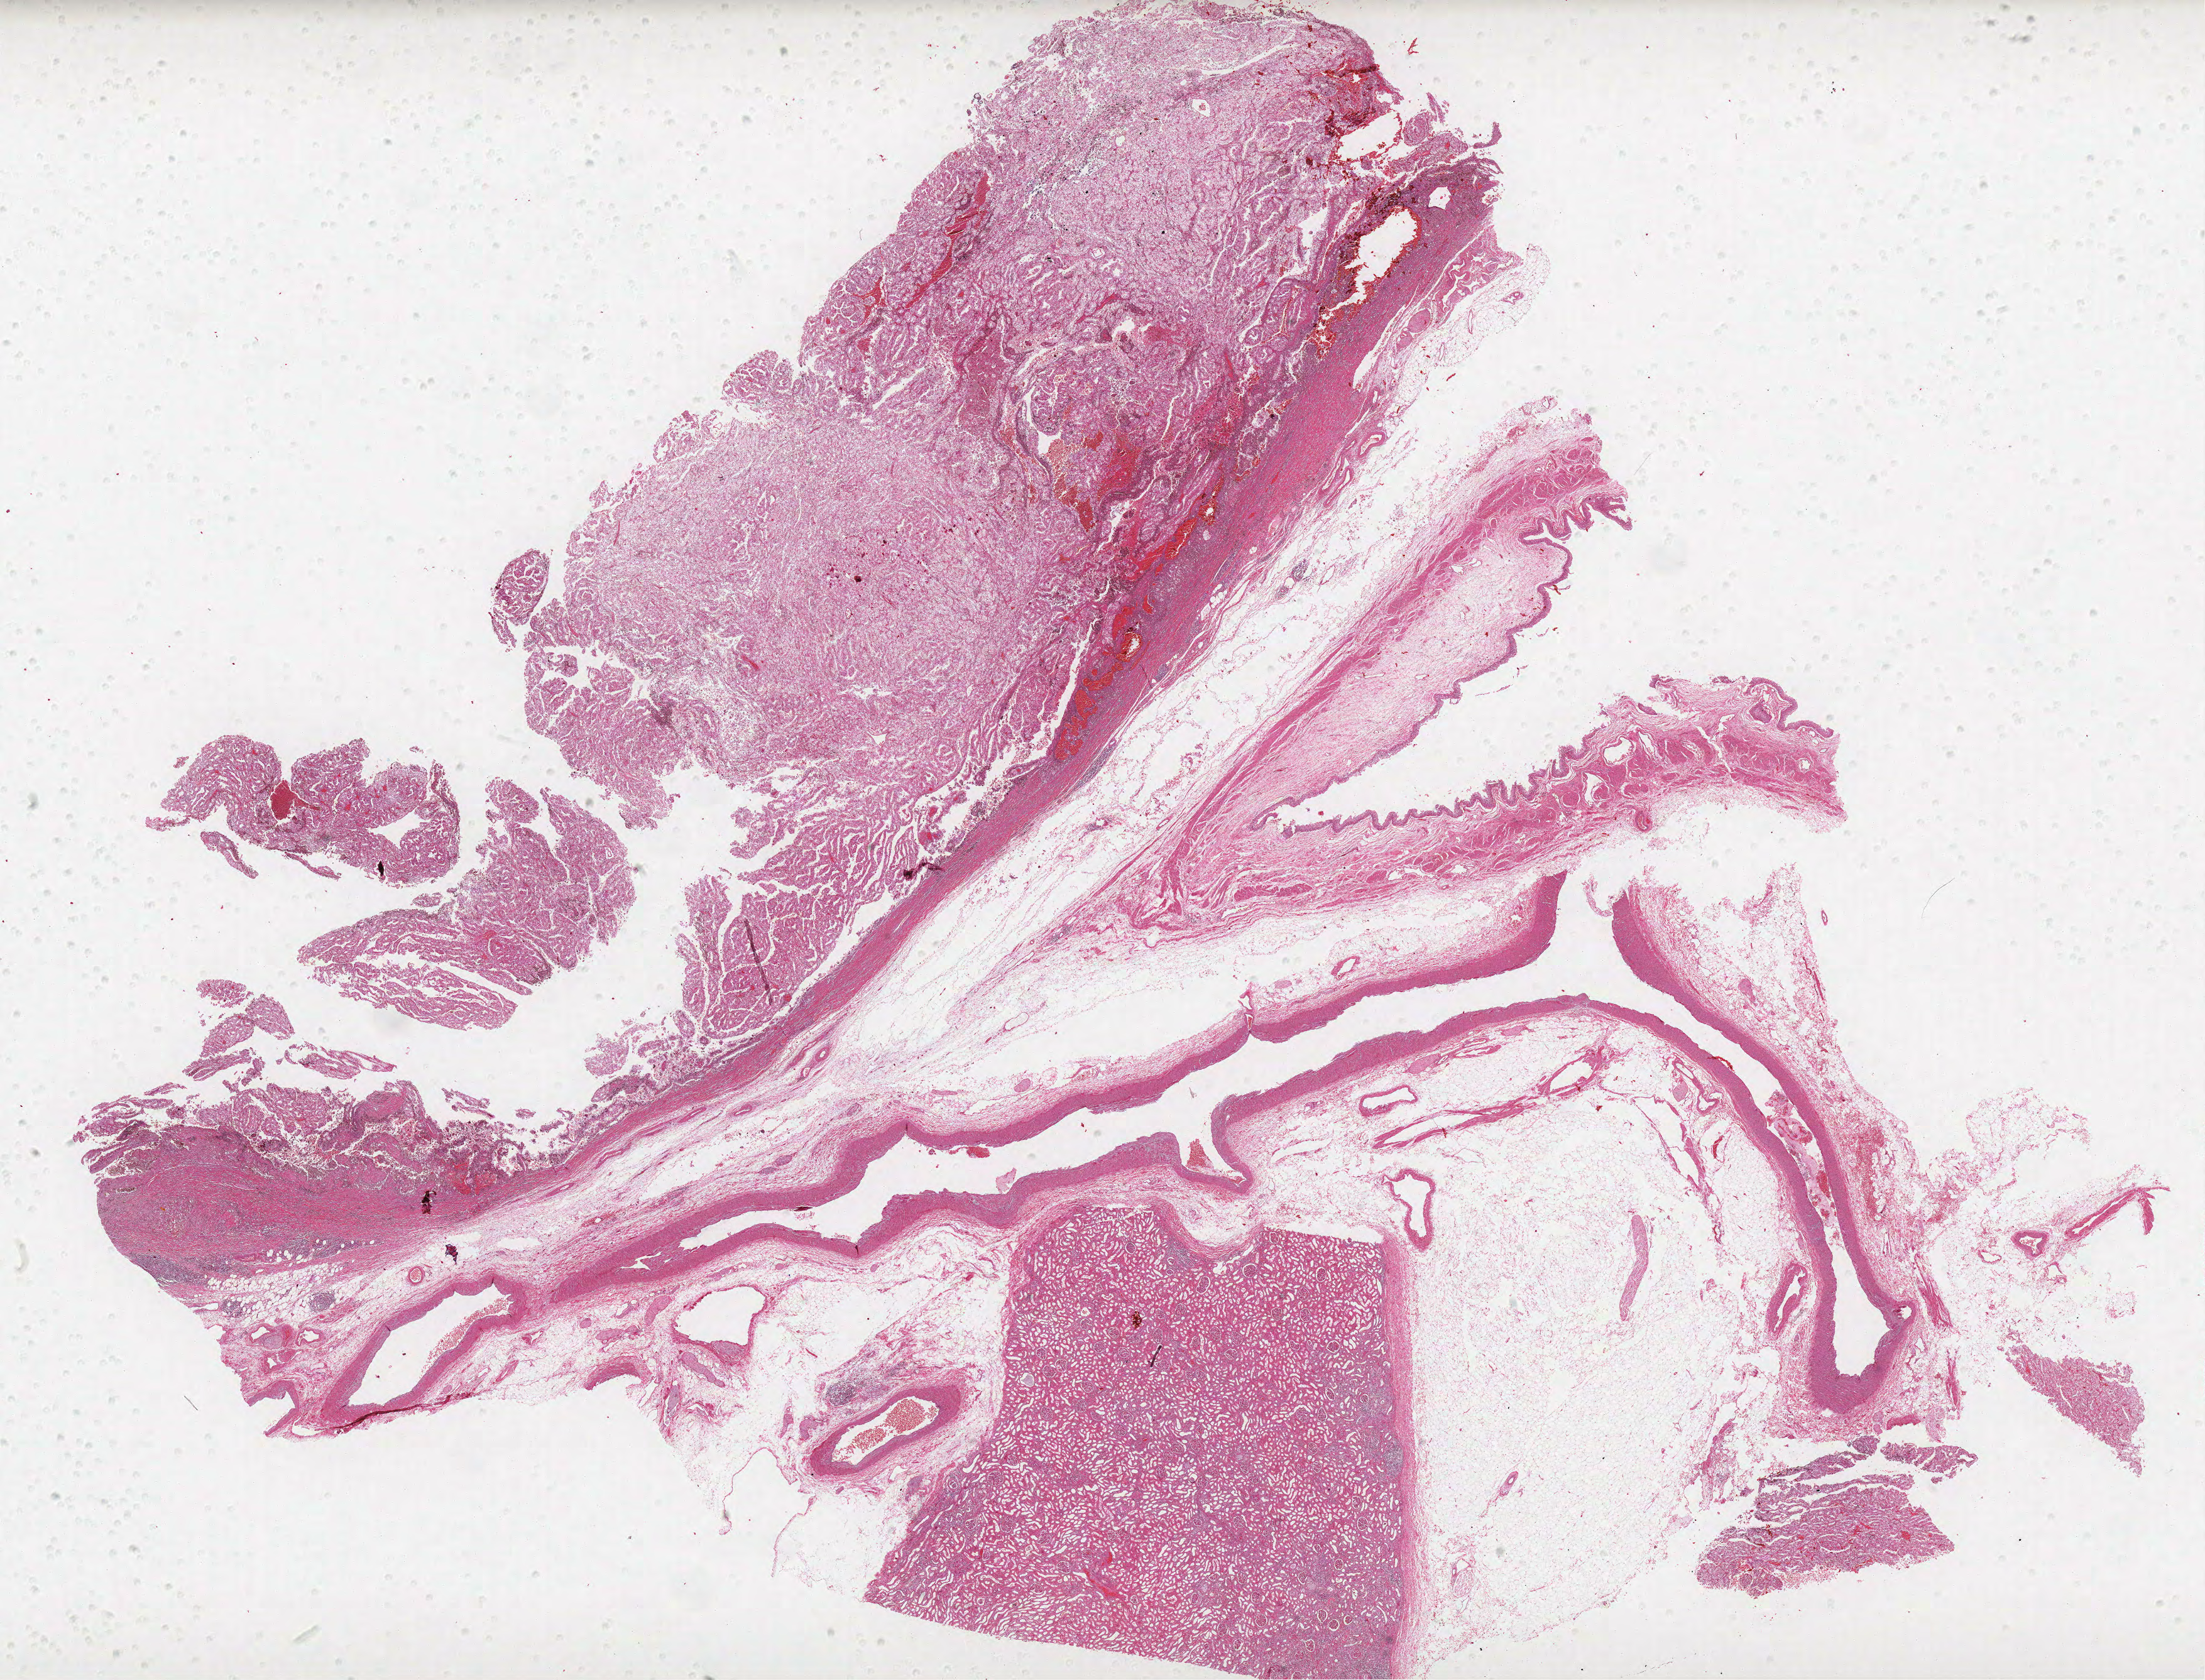
Whole-slide histology image, Hematoxylin and eosin (H&E) stained — shown as a low-resolution overview of the whole scanned area (about 28.1 x 21.4 mm, acquisition: 40x scan), FFPE section, kidney, primary tumour sample. Female, age 62 years at initial diagnosis. Histologic grade: G2 (moderately differentiated).
* diagnosis: Clear cell adenocarcinoma, NOS
* TNM: T1b N0 M0
* AJCC pathologic stage: I